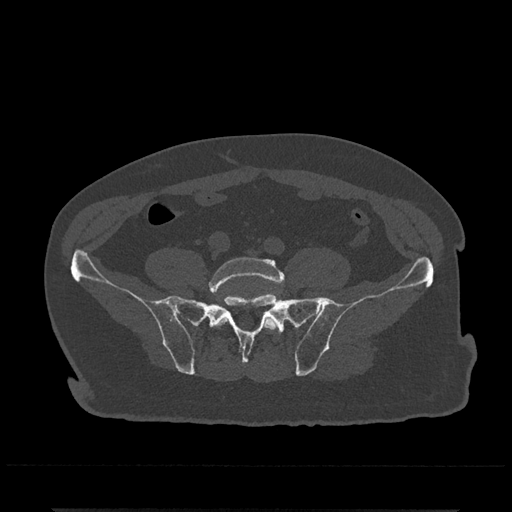
CT including the spine, one axial slice. Slice 50 of 797 in the series (ordered by position). Reconstruction kernel Br40s/3. 120 kVp. Bone window (W 1800 / L 400 HU). 0.5 mm slice thickness. 512 × 512 image matrix, field of view 393 × 393 mm. Patient: male, 67 years. Case-level facts recorded for this patient, not image findings: primary cancer: prostate.
Annotated regions visible in this slice (semi-automatic segmentation, software-assisted and operator-edited):
- L5 vertebra: bounding box <209,257,285,331> (left, top, right, bottom; pixels)